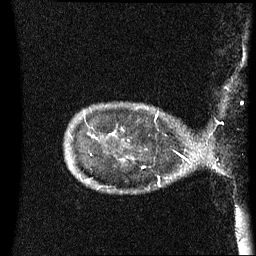
Breast MRI (dynamic contrast-enhanced), one sagittal slice; position 10 of 60 along the scan axis; dynamic contrast-enhanced series, image 2 of 3 at this slice position (ordered by acquisition); 1.5 T; TE 4.2 ms, TR 8.4 ms; 2.5 mm slice thickness; 256 × 256 image matrix, field of view 220 × 220 mm. Female patient, age 41 years. From the clinical record (not read from this slice): setting: breast cancer imaged before/during neoadjuvant chemotherapy; receptor status: HER2-positive.
Outlined on this slice (semi-automatically segmented with operator editing):
- analysis volume of interest (the breast-tissue region the enhancement analysis was run in; not a lesion): bounding box (x1, y1, x2, y2) in pixels: (122, 104, 190, 137)
- tumour enhancement mask (voxels above the 70 % enhancement threshold inside the analysis volume of interest): (155, 118, 157, 121)